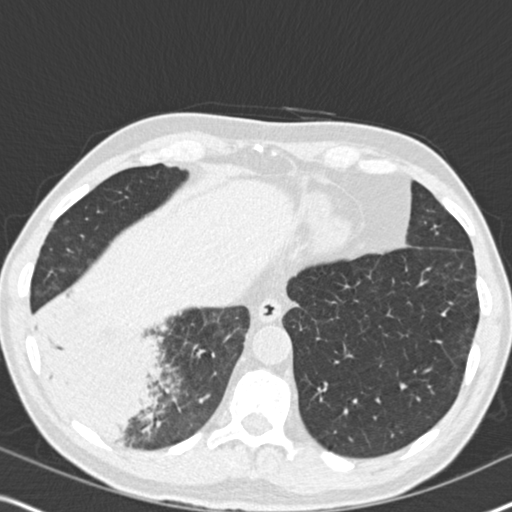
Low-dose screening chest CT, one axial slice; slice 56 of 182 in the series (ordered by position); 120 kVp; lung window (W 1500 / L -600 HU); 512 × 512 image matrix, field of view 330 × 330 mm.
Annotated regions visible in this slice (expert manual segmentation):
- lesion 1 (tumor, lower lobe of right lung): bounding box <41,325,158,438> (left, top, right, bottom; pixels)